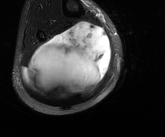
MRI of an extremity soft-tissue mass, one axial slice; T2-weighted fat-saturated; MR volume resampled by the dataset authors to the PET/CT grid (not the native acquisition matrix); 165 × 137 image matrix, field of view 161 × 134 mm. Male patient. From the clinical record (not read from this slice): histological type: liposarcoma - round cell; grade: high; site of the primary tumour: right calf.
Annotated regions visible in this slice (expert contour drawn on MRI and transferred to this co-registered scan by the dataset authors):
- gross tumour volume (mass): bounding box <23,21,111,99> (left, top, right, bottom; pixels)